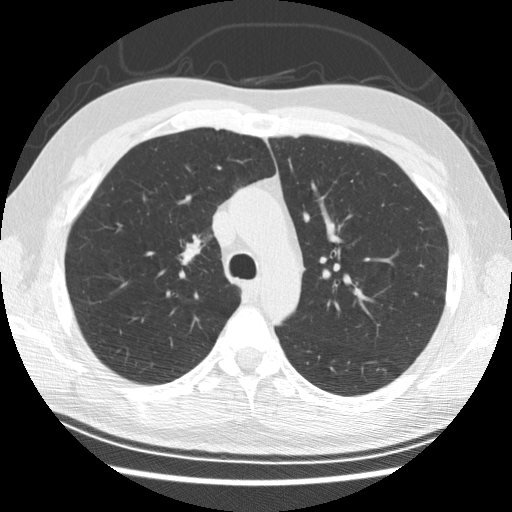
Chest CT (low-dose screening protocol), one axial image. First (baseline) screen. Lung window (W 1500 / L -600 HU). 2.5 mm slice thickness. Male participant, aged 57 years at enrolment. Former smoker at enrolment.
Expert-annotated lung lesion, bounding box [x1, y1, x2, y2] px = [164, 221, 222, 279]. The screening reader recorded 6 non-calcified nodules or masses ≥4 mm on this exam (right middle lobe, right middle lobe, right lower lobe, right middle lobe, right middle lobe, right lower lobe); which of them this box marks is not recorded. Later outcome: lung cancer diagnosed 766 days after this screen (after the second annual screen) — adenocarcinoma, NOS, right upper lobe, poorly differentiated (G3), stage IB (AJCC 6th edition), 25 mm at pathology.